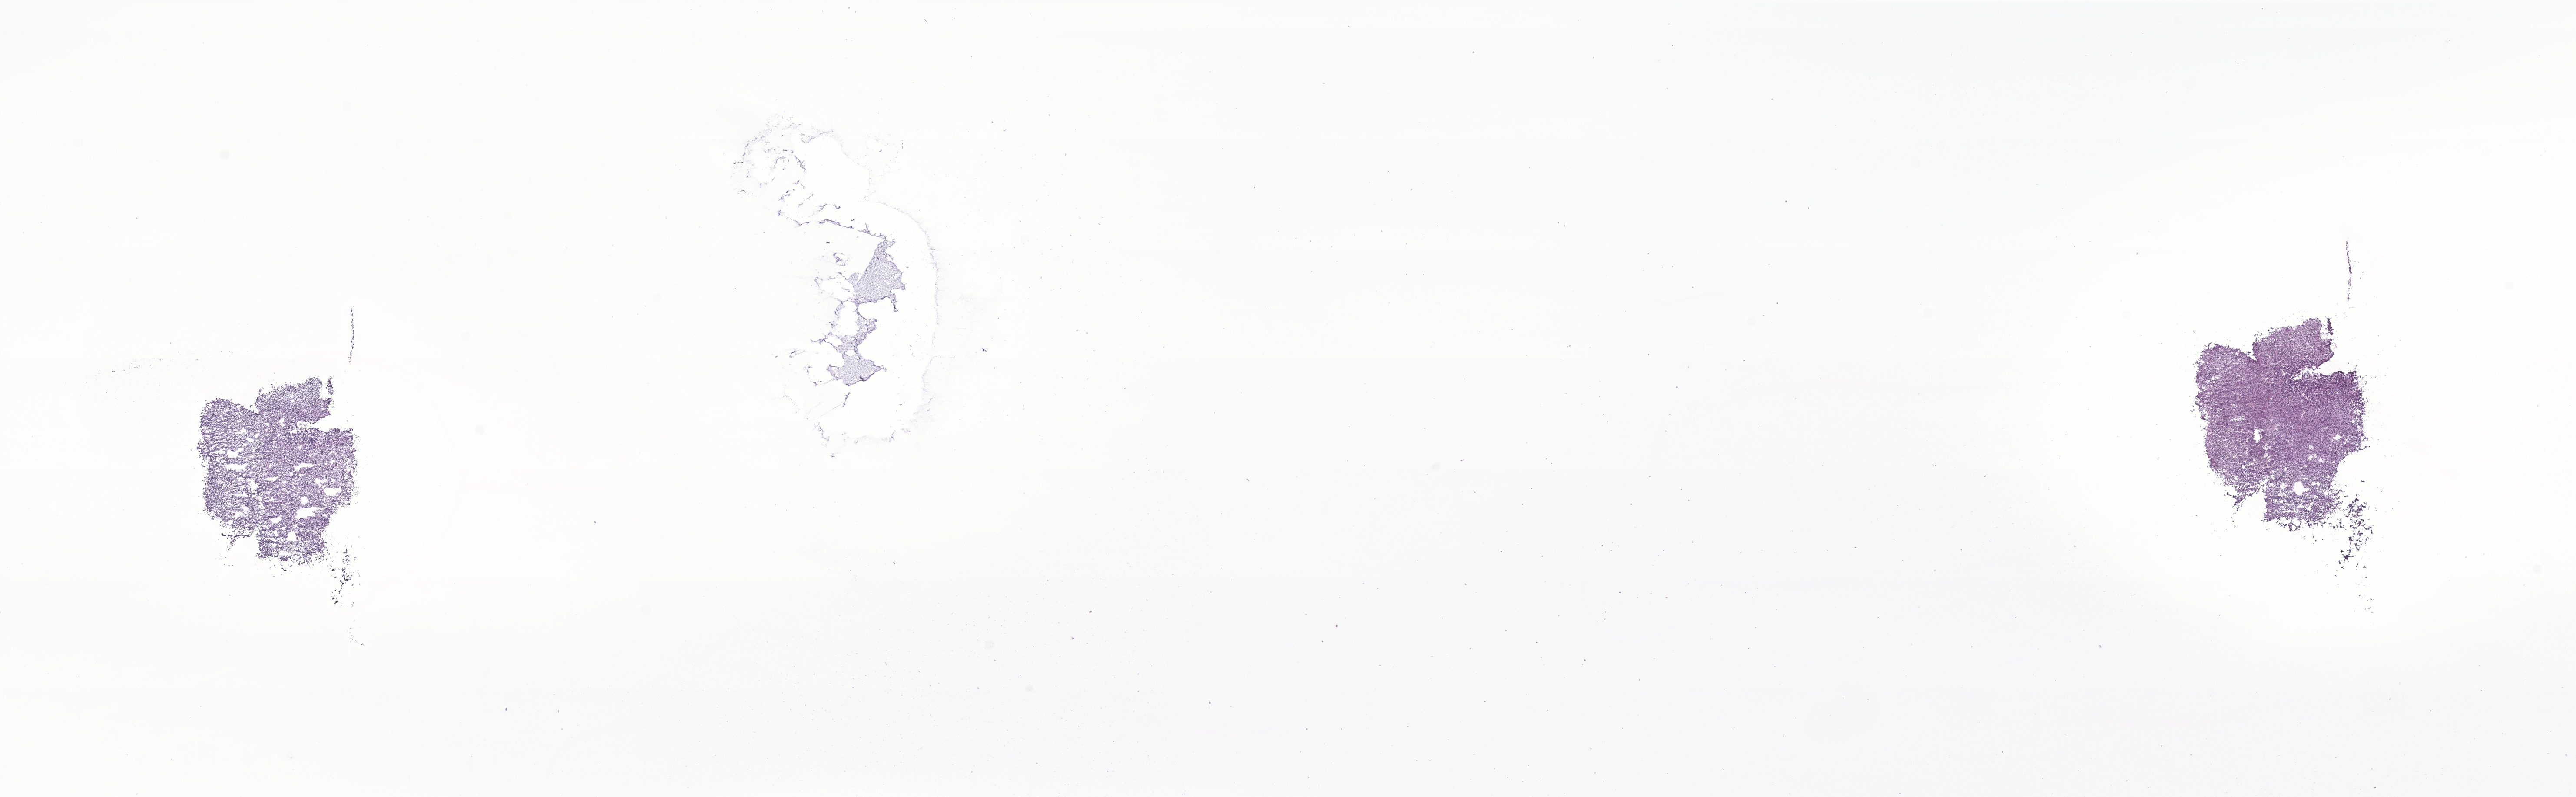
Digitized hematoxylin and eosin (H&E)-stained section of tumor tissue from the cerebellum, low-resolution overview of the scanned area, about 25.0 x 7.7 mm, cryosection (OCT / tissue freezing medium). Patient female; age 42 months (3 years 6 months).
* recorded diagnosis: Medulloblastoma, NOS